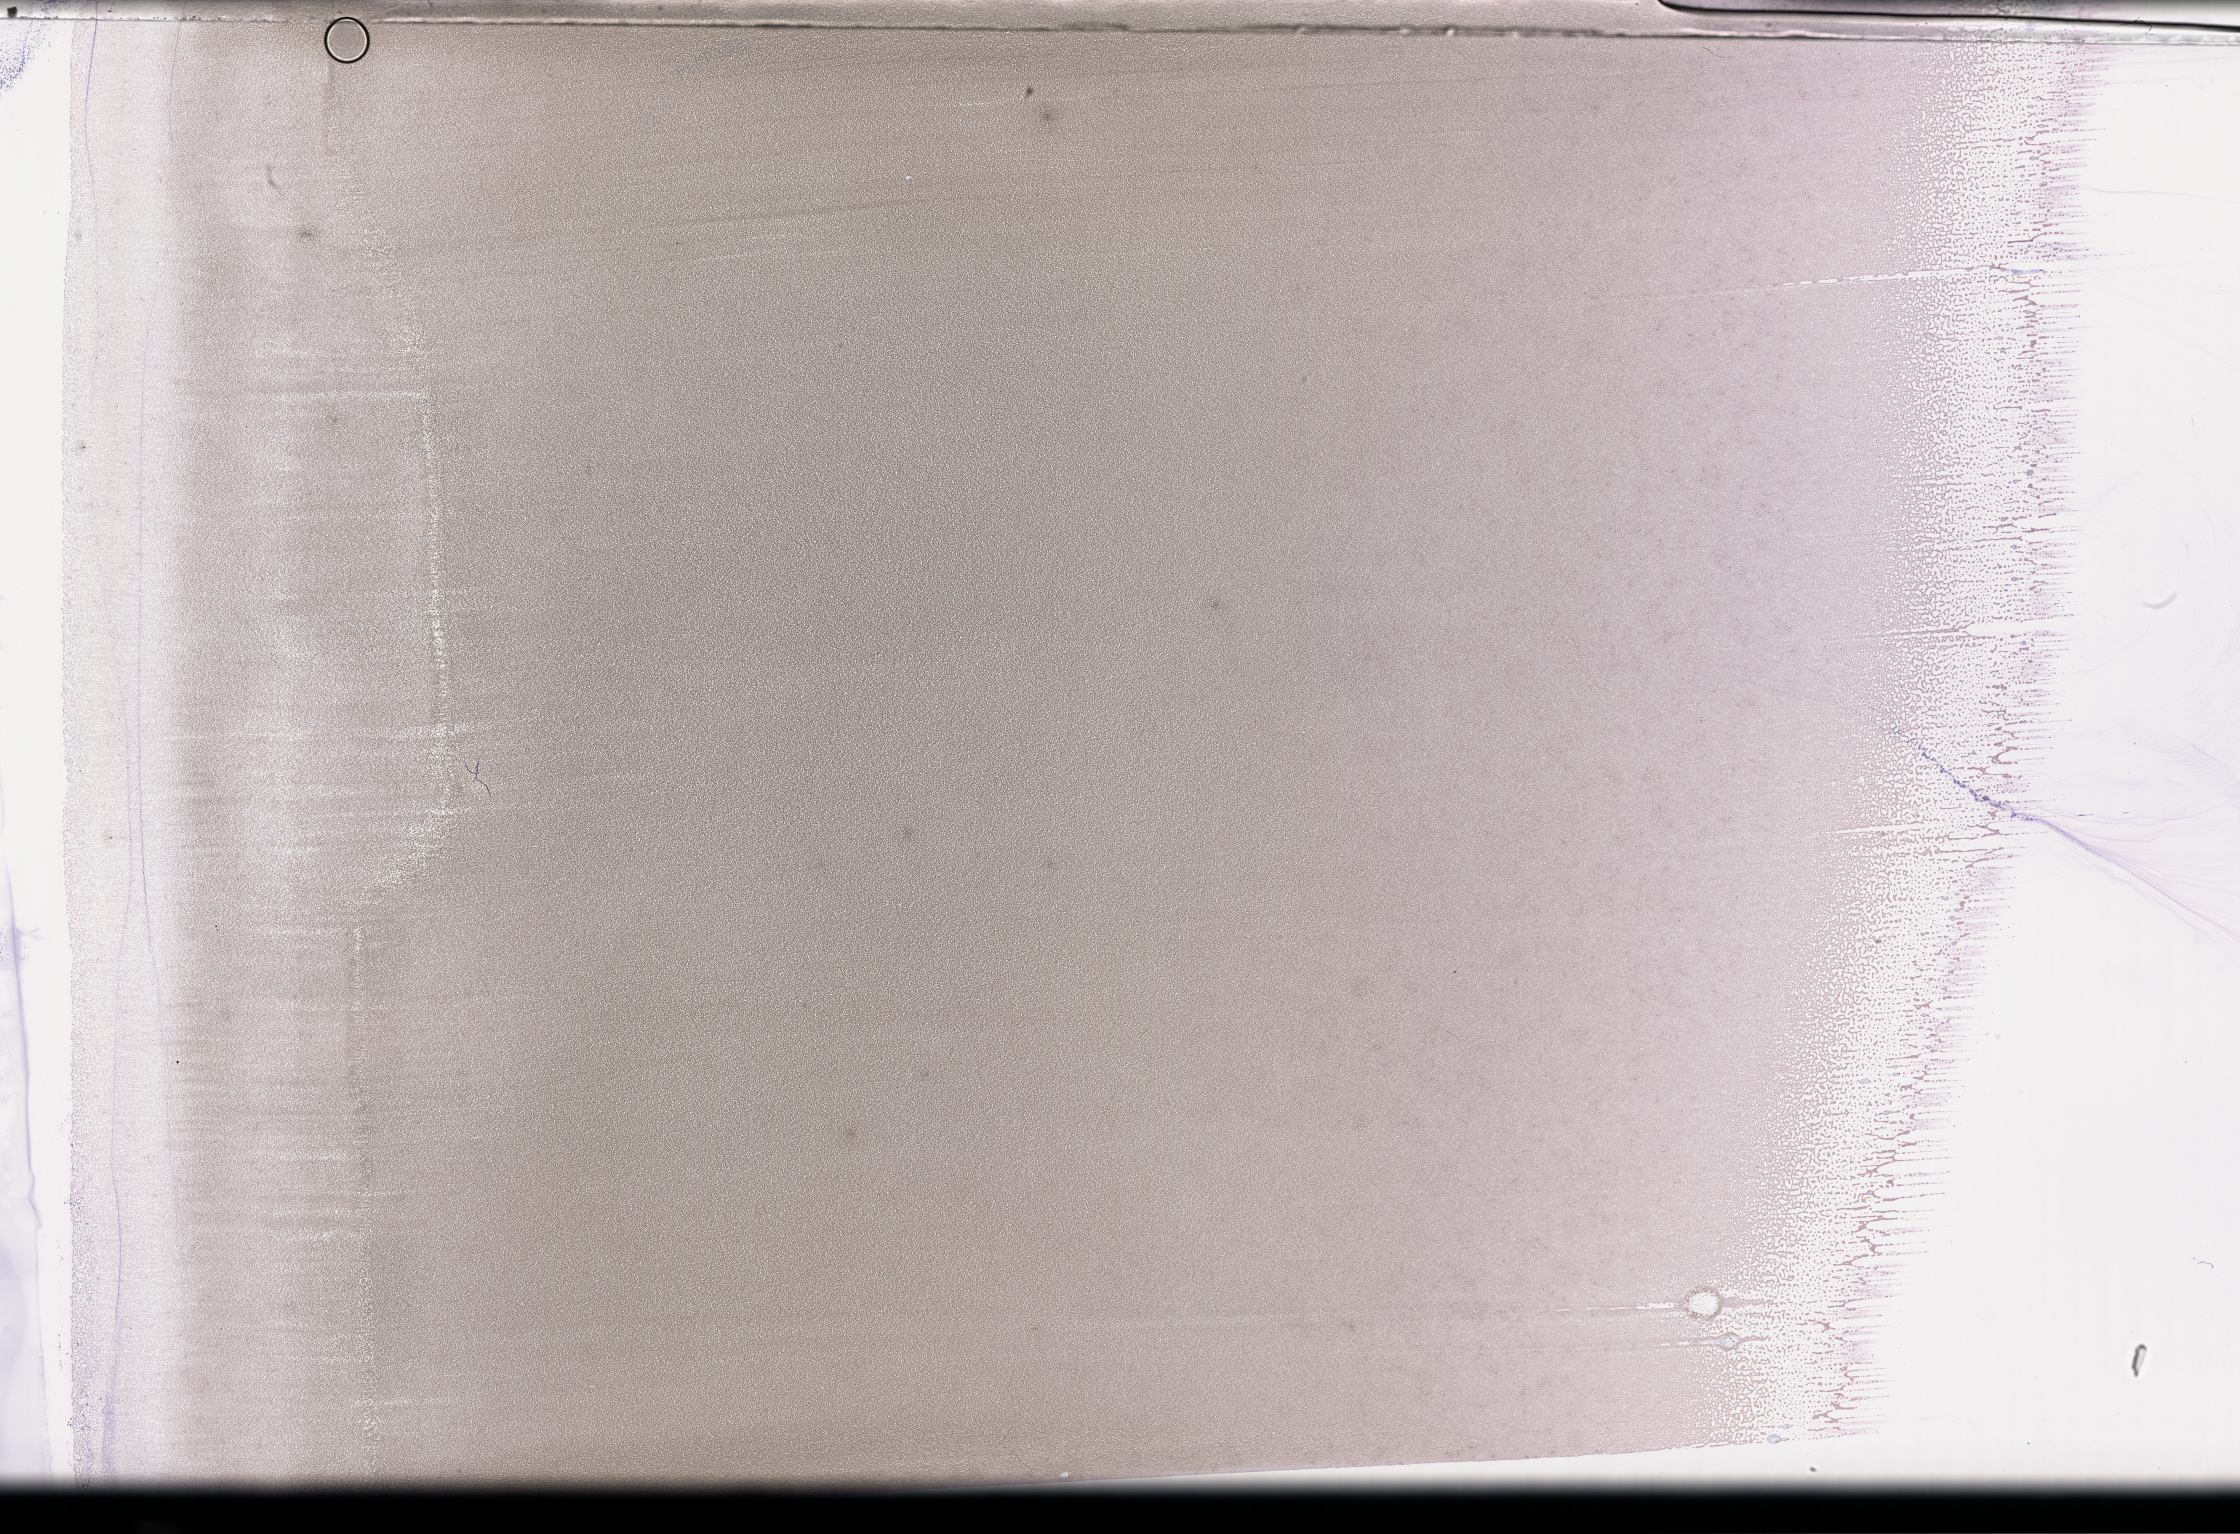
Whole-slide image of a whole blood smear, Wright–Giemsa stain, a low-resolution overview of the entire scanned area, about 36.2 x 24.8 mm. Collected on treatment. Male patient.
- patient diagnosis: Plasma Cell Myeloma